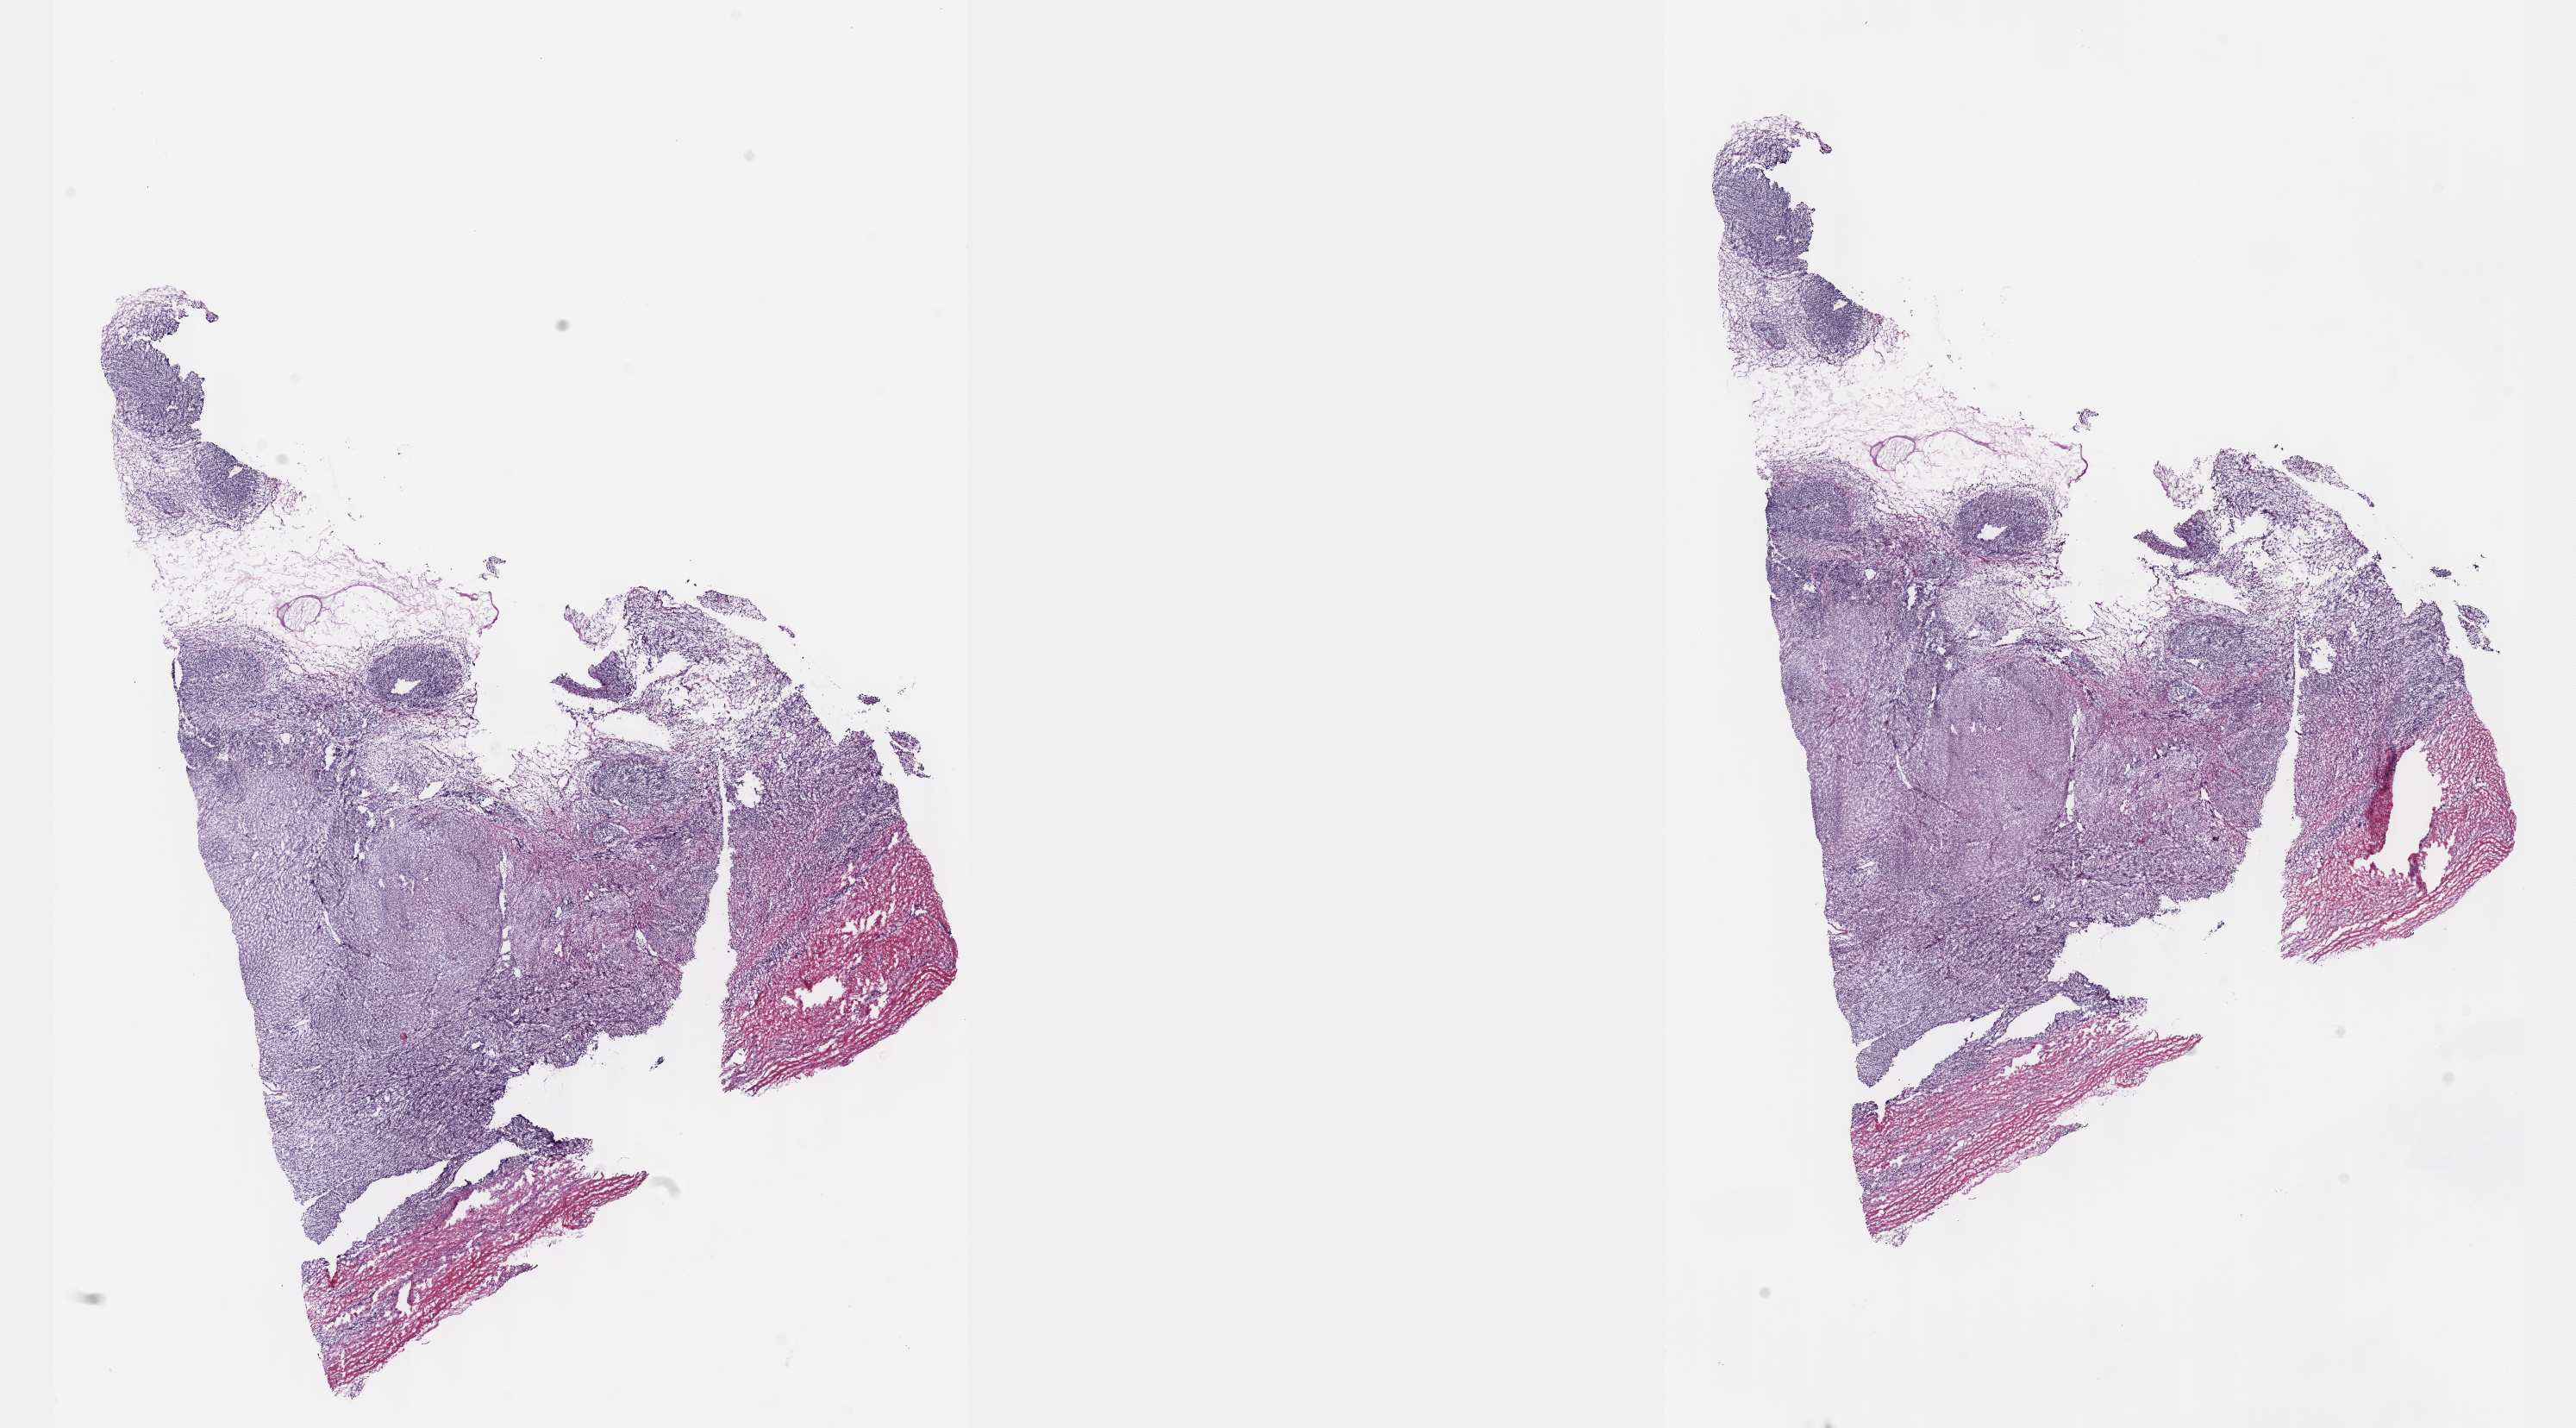
Digitized H&E tissue section (whole slide) — shown as a low-resolution overview of the whole scanned area (about 24.1 x 13.4 mm). Frozen section from the top of the tissue portion. Sample: primary tumour, connective, subcutaneous and other soft tissues. Female patient; age at initial diagnosis 20 years. Pathologist review of this section (percent, as recorded): tumour cells 80%, tumour nuclei 100%, normal cells 0%, stromal cells 20%, necrosis 0%. Infiltration values recorded for this section: lymphocyte infiltration 0%, monocyte infiltration 0%, neutrophil infiltration 0%.
Pathologic diagnosis: Malignant peripheral nerve sheath tumor (connective, subcutaneous and other soft tissues of lower limb and hip).